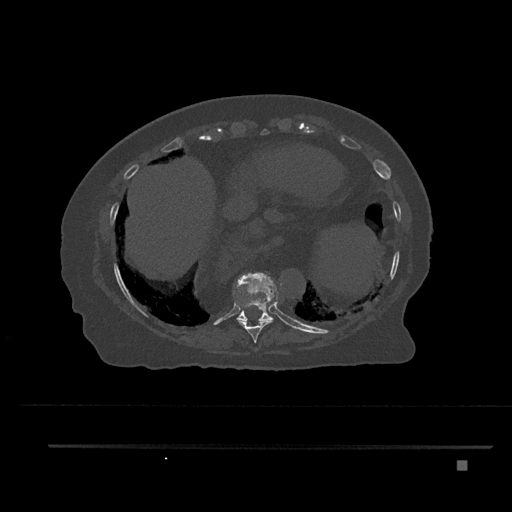
CT including the spine, one axial slice; position 379 of 797 along the scan axis; reconstruction kernel Br40s/3; 120 kVp; bone window (W 1800 / L 400 HU); 512 × 512 image matrix, field of view 437 × 437 mm. Patient: female, 76 years. Case-level facts recorded for this patient, not image findings: primary cancer: lung; vertebrae with lytic lesions (as recorded): T11, L3.
Outlined on this slice (semi-automatically segmented with operator editing):
- T10 vertebra: bounding box <237,272,275,322> (left, top, right, bottom; pixels)
- T8 vertebra: <255,348,257,350>
- T9 vertebra: <234,296,271,343>